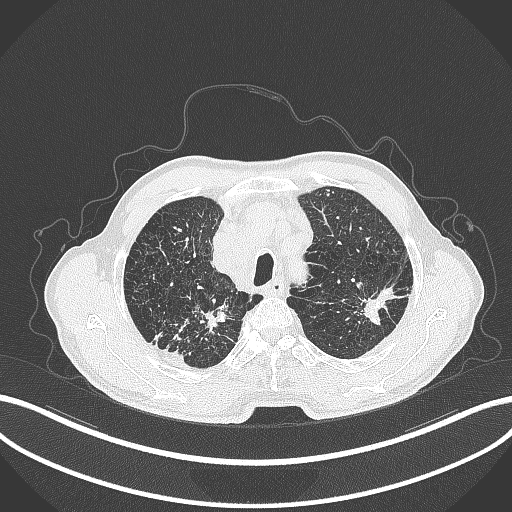
Chest CT, one axial slice; slice 365 of 463 in the series (ordered by position); 120 kVp; lung window (W 1500 / L -600 HU); 1 mm slice thickness; 512 × 512 image matrix. Male patient, age 74 years. Case-level facts recorded for this patient, not image findings: clinical TNM (as recorded): T2a N1 M0.
Annotated regions visible in this slice (rectangle marked by the reading radiologist):
- lung tumour (recorded histology: adenocarcinoma): bounding box [x1, y1, x2, y2] px = [355, 279, 399, 331]